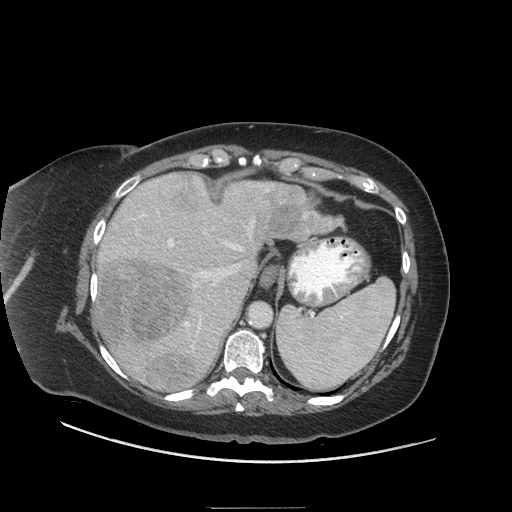
Contrast-enhanced abdominal CT (liver protocol), one axial slice. Position 47 of 81 along the scan axis. Reconstruction kernel STANDARD. 140 kVp. Soft-tissue window (W 400 / L 40 HU). 512 × 512 image matrix. Case-level facts recorded for this patient, not image findings: diagnosis: hepatocellular carcinoma (patient treated with transarterial chemoembolisation; whether this scan precedes or follows treatment is not stated here); TNM stage (as recorded): Stage-II; Child-Pugh class: A; tumour differentiation: moderately differentiated; tumour nodularity: multinodular.
Outlined on this slice (semi-automatic segmentation, software-assisted and operator-edited):
- liver parenchyma outside the tumour (the mass and vessels are separate outlines, so this box may not span the whole liver): bounding box [x1, y1, x2, y2] px = [92, 172, 297, 390]
- mass: [97, 174, 337, 392]
- liver vessels: [94, 180, 269, 353]